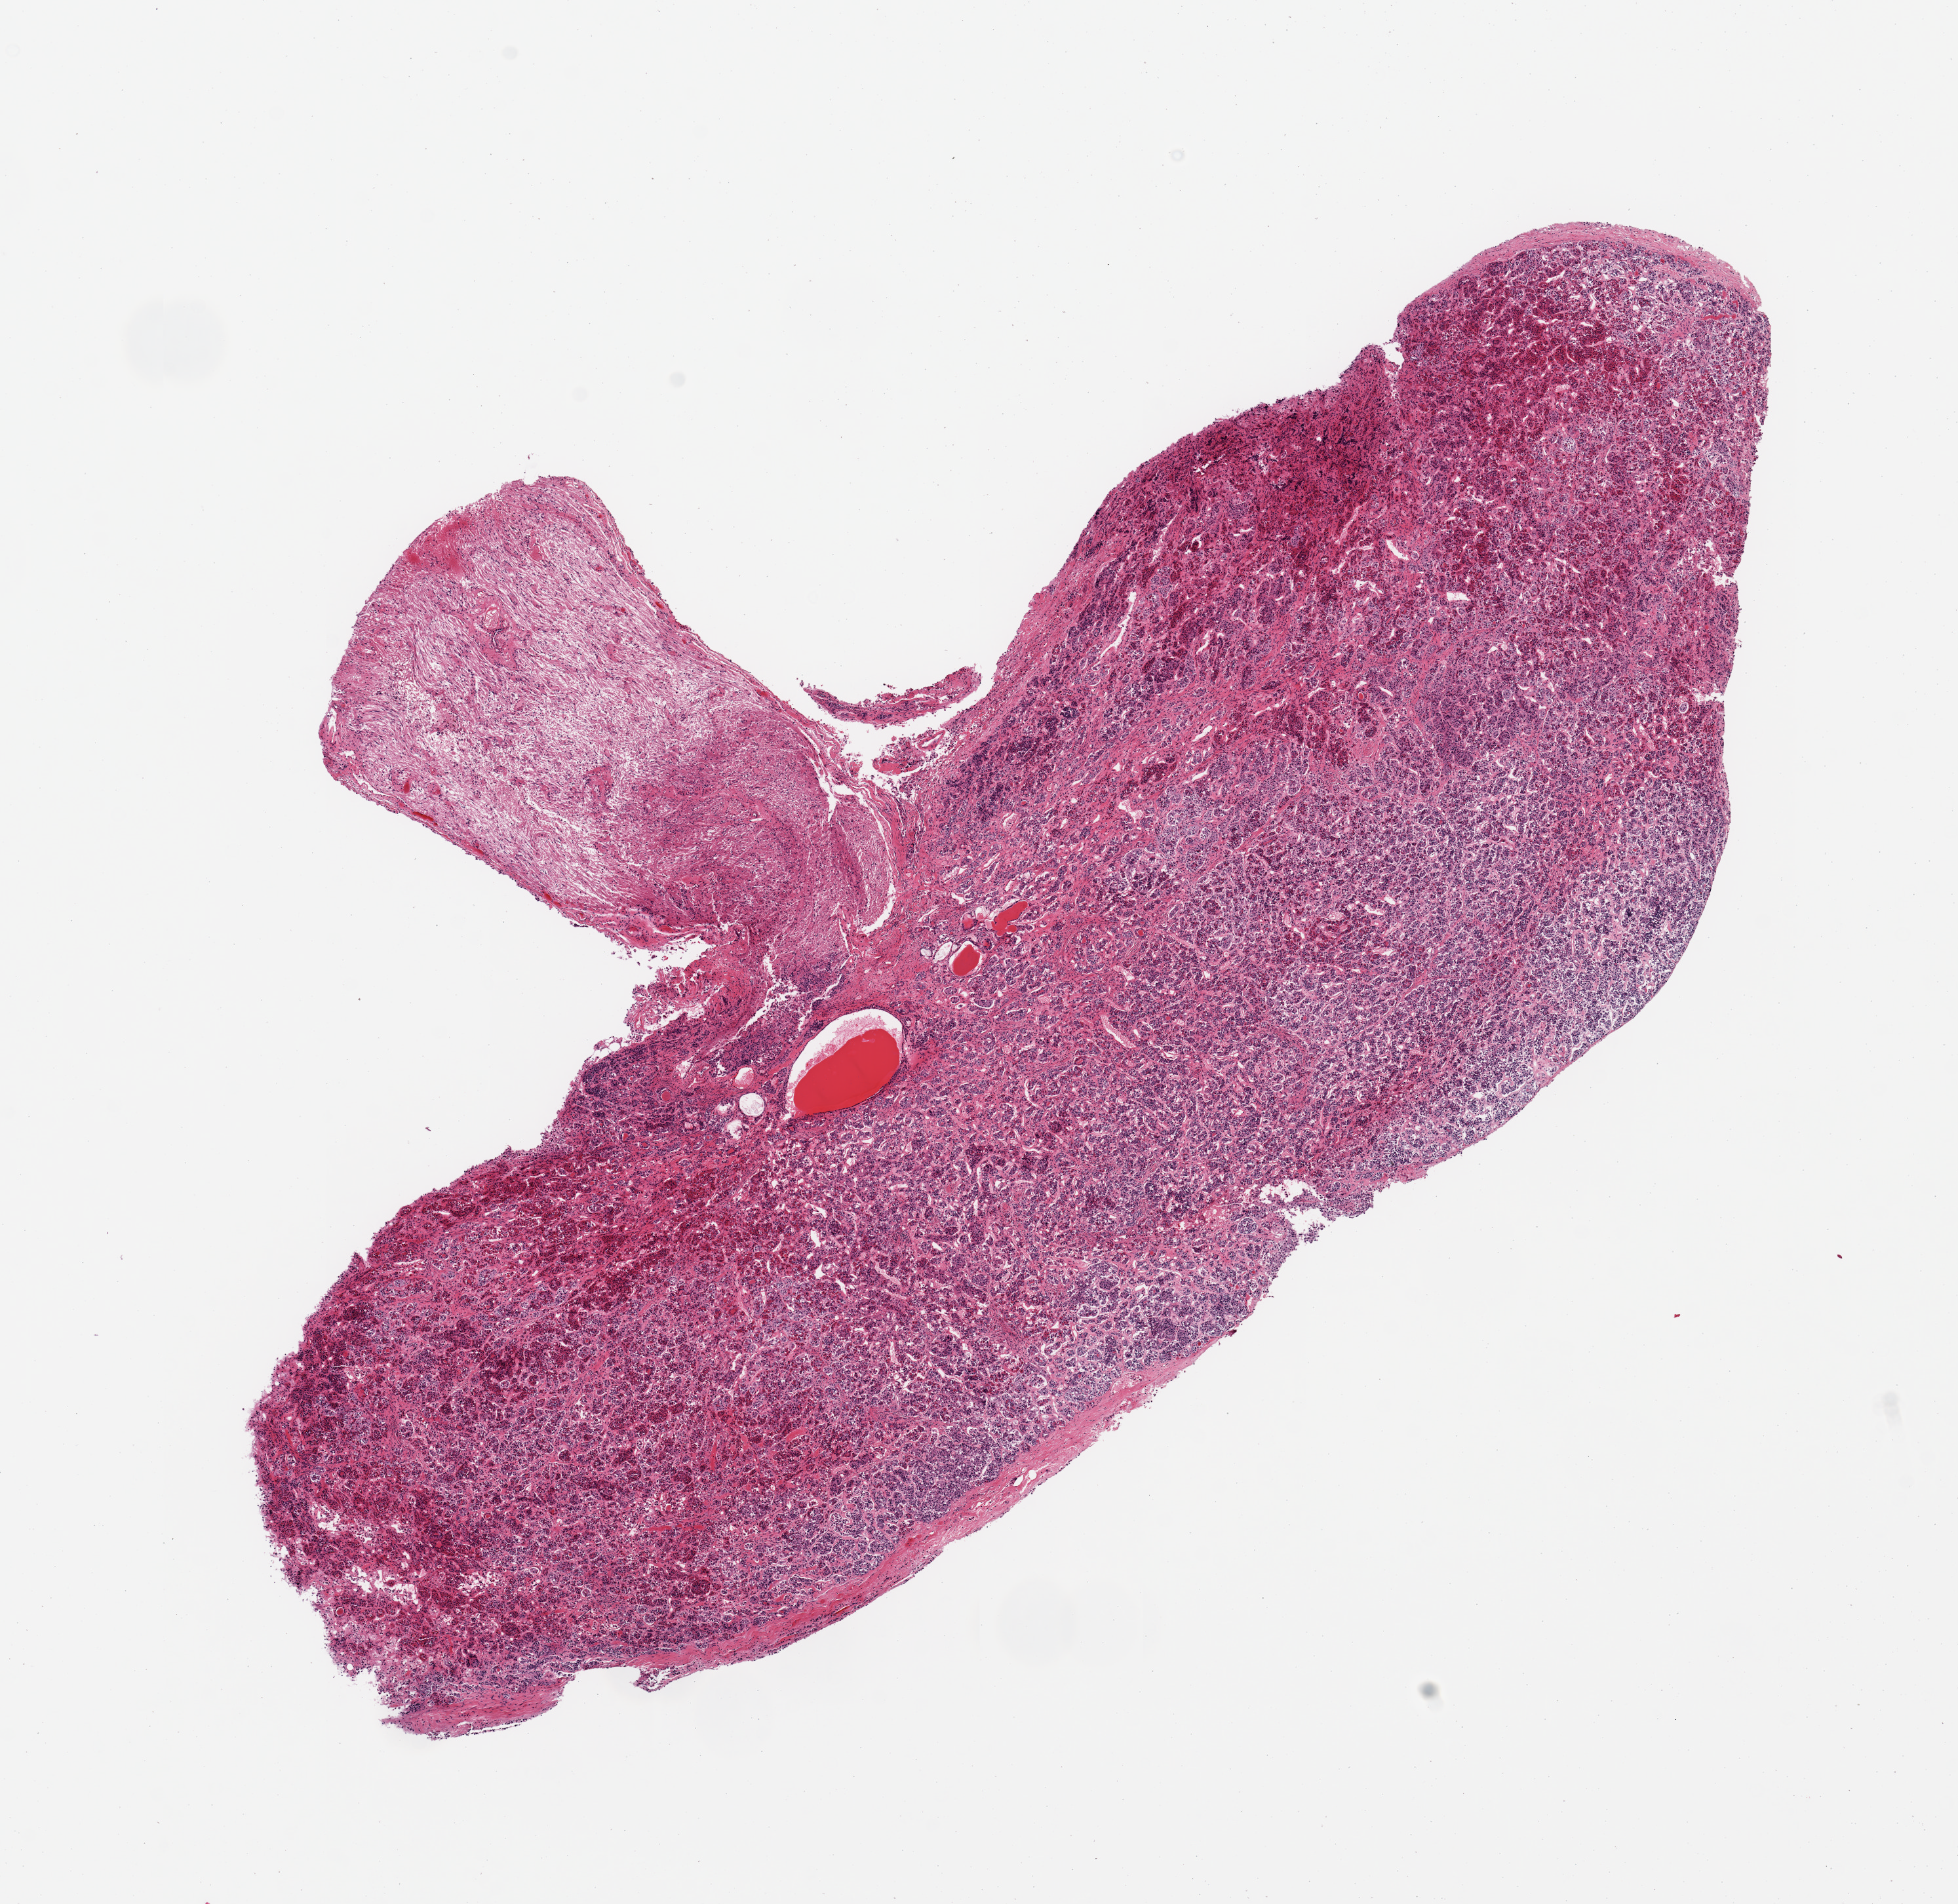
Digitized haematoxylin and eosin-stained section — a low-resolution overview of the entire scanned area, about 11.8 x 11.5 mm (slide scanned at 20x). PAXgene-fixed, paraffin-embedded tissue. Target tissue: pituitary. Donor tissue sample. Male donor.
Pathologist's review note for this sample: 1 piece; well dissected with anterior and posterior lobes well defined.